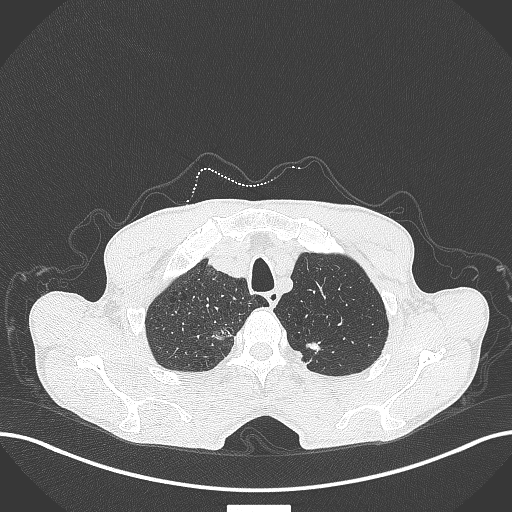
Chest CT, one axial slice. Position 376 of 445 along the scan axis. Lung window (W 1500 / L -600 HU). 1 mm slice thickness. 512 × 512 image matrix, field of view 400 × 400 mm. Patient: male, 70 years. Case-level facts recorded for this patient, not image findings: clinical TNM (as recorded): T1a N0 M0; histopathological grade: G1-2.
Outlined on this slice (rectangle marked by the reading radiologist):
- lung tumour (recorded histology: adenocarcinoma): bounding box (x1, y1, x2, y2) in pixels: (208, 321, 234, 342)